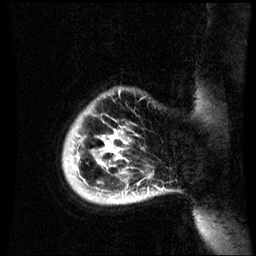
Breast MRI (dynamic contrast-enhanced), one sagittal slice. Position 7 of 60 along the scan axis. Dynamic contrast-enhanced series, image 2 of 3 at this slice position (ordered by acquisition). 1.5 T. TE 4.2 ms, TR 8.9 ms. 2.6 mm slice thickness. 256 × 256 image matrix, field of view 220 × 220 mm. Female patient, age 35 years. From the clinical record (not read from this slice): setting: breast cancer imaged before/during neoadjuvant chemotherapy; receptor status: HR-positive, HER2-negative.
Outlined on this slice (semi-automatic segmentation, software-assisted and operator-edited):
- analysis volume of interest (the breast-tissue region the enhancement analysis was run in; not a lesion): bounding box (x1, y1, x2, y2) in pixels: (62, 88, 164, 205)
- tumour enhancement mask (voxels above the 70 % enhancement threshold inside the analysis volume of interest): (97, 130, 128, 199)